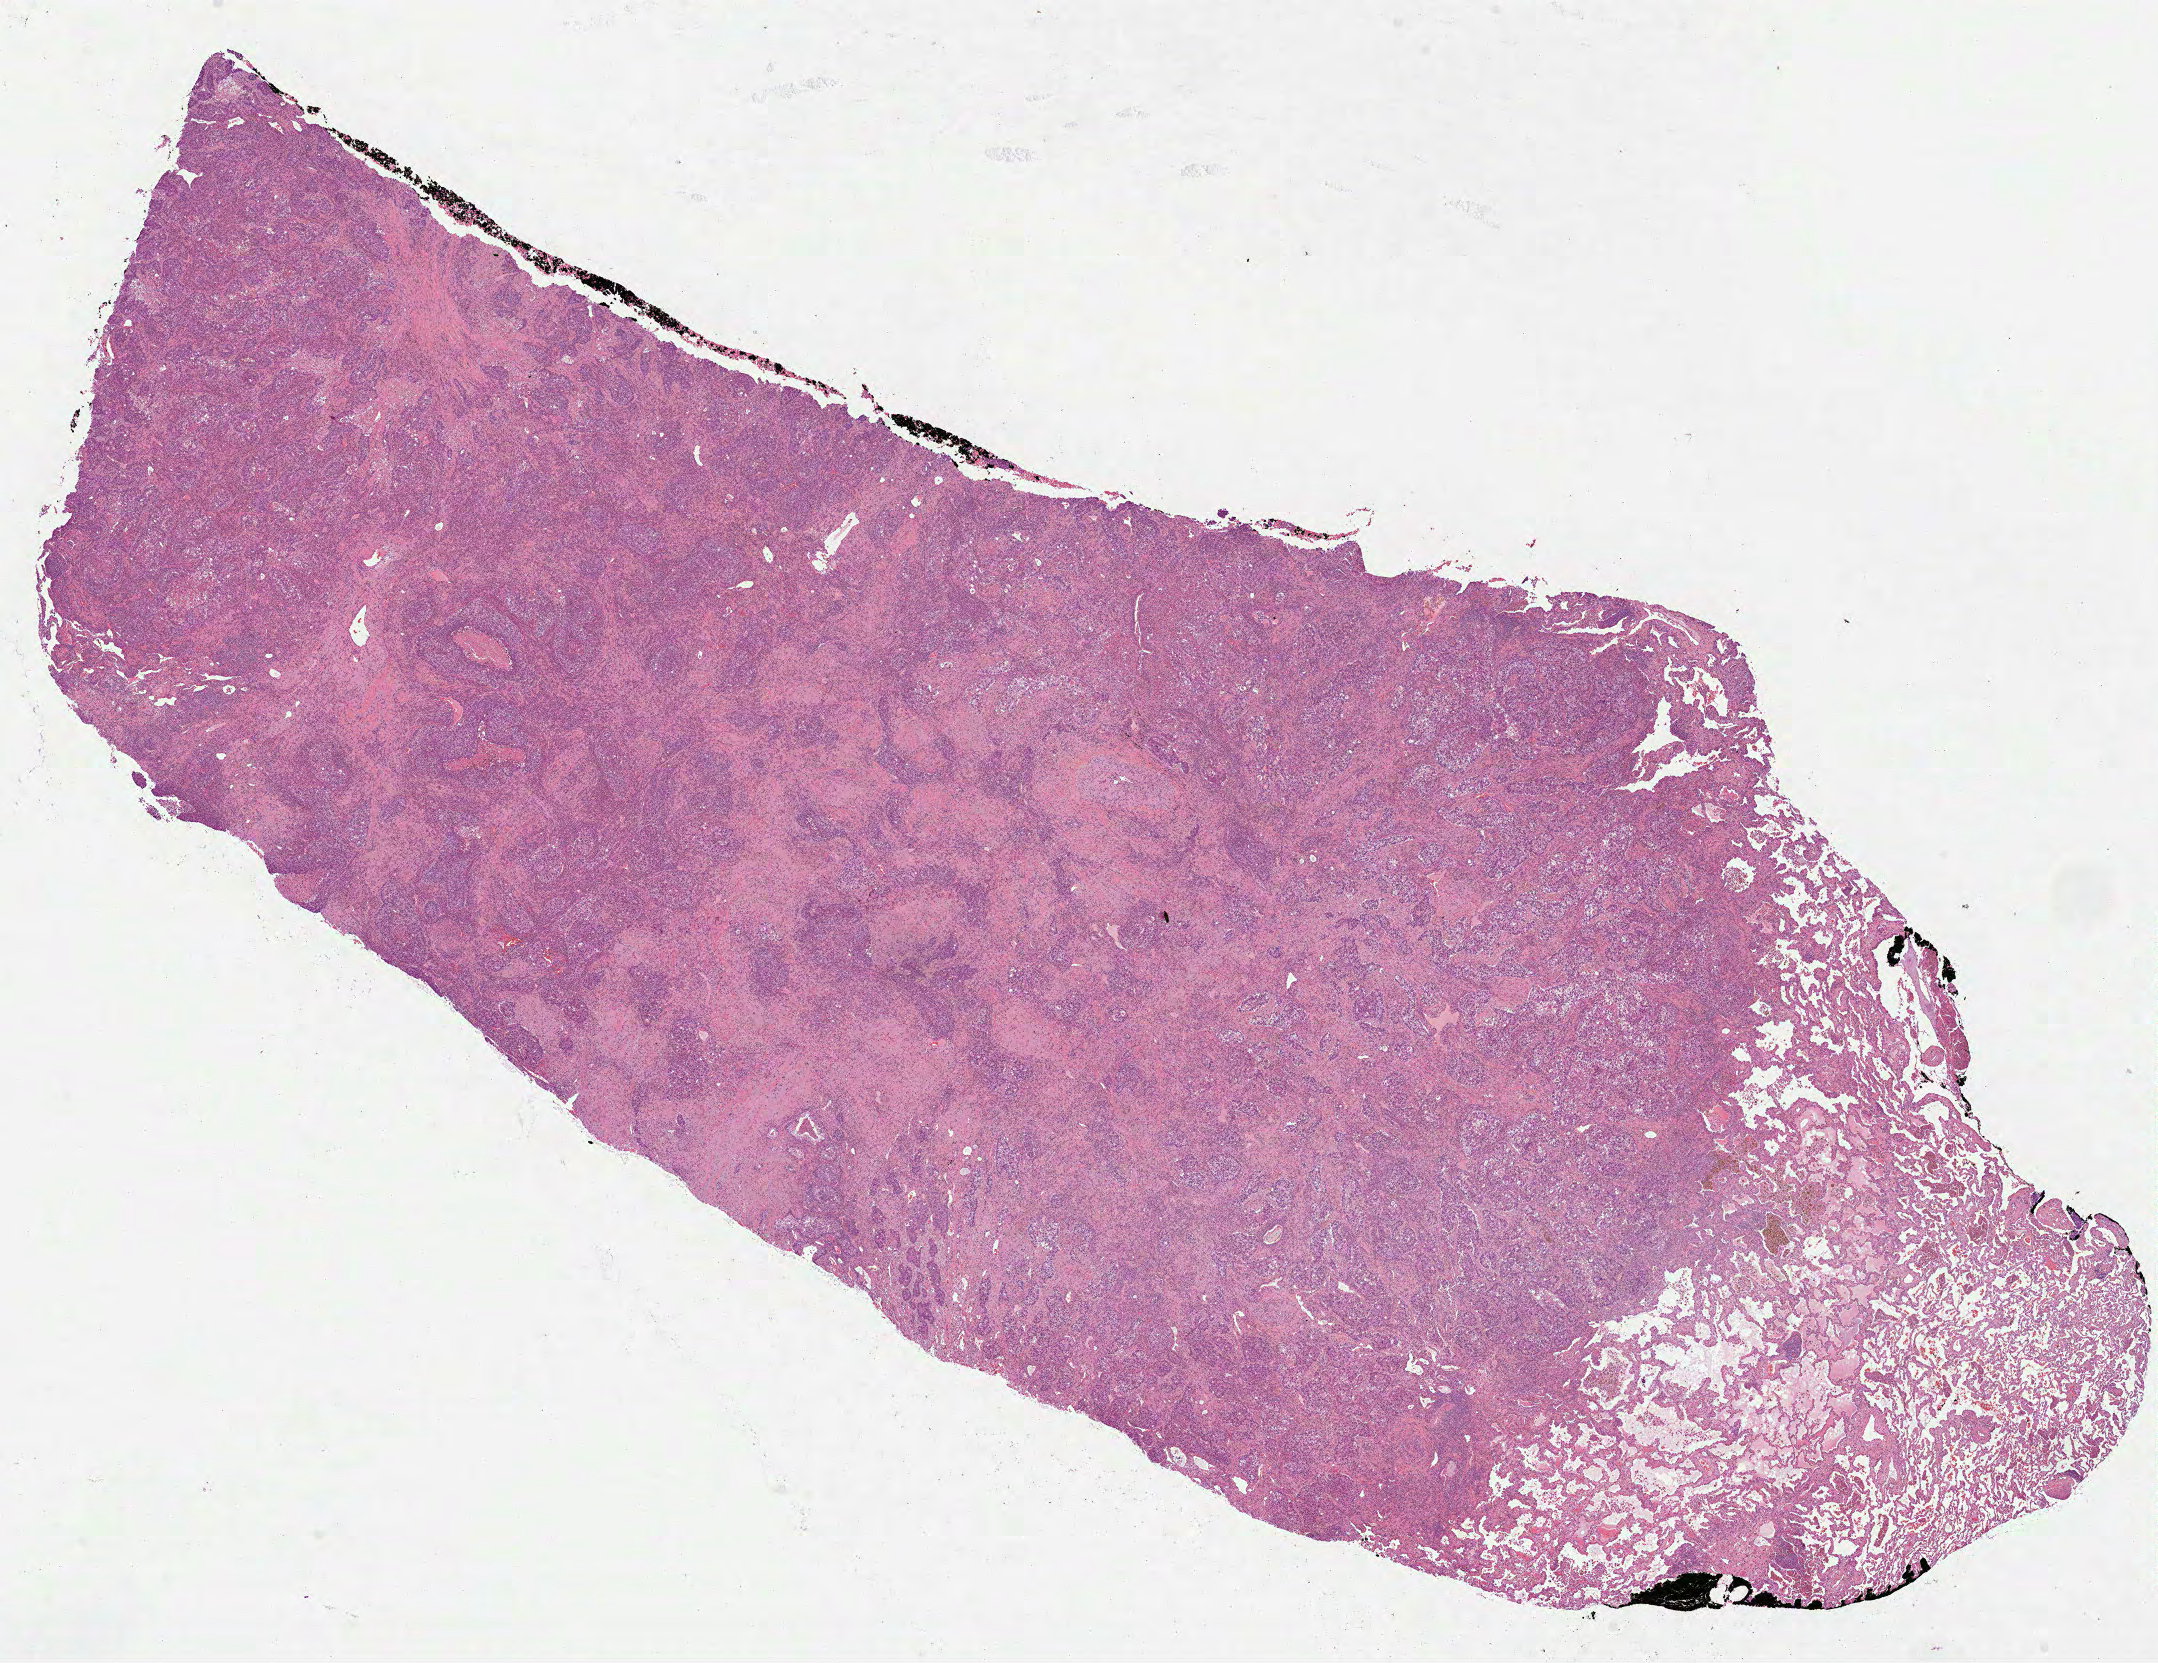
Digitized H&E tissue section (whole slide) — a low-resolution overview of the entire scanned area, about 17.4 x 13.4 mm (acquisition: 40x scan), formalin-fixed paraffin-embedded (FFPE) diagnostic section, sample: primary tumour, lung. Male patient; age at initial diagnosis 52 years.
- pathologic diagnosis: Adenocarcinoma, NOS (upper lobe, lung)
- laterality: left
- AJCC pathologic stage: IB (6th edition)